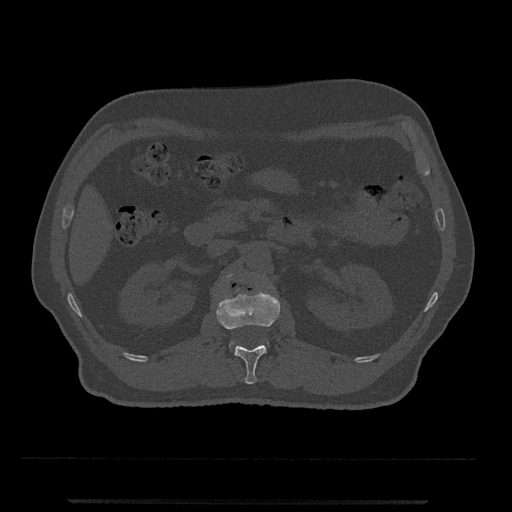
CT including the spine, one axial slice; position 314 of 797 along the scan axis; reconstruction kernel Br40s/3; 120 kVp; bone window (W 1800 / L 400 HU); 0.5 mm slice thickness; 512 × 512 image matrix. Male patient, age 63 years. Case-level facts recorded for this patient, not image findings: primary cancer: prostate.
Outlined on this slice (semi-automatically segmented with operator editing):
- L1 vertebra: box from (x=216, y=288) to (x=280, y=384) px
- L2 vertebra: (x=227, y=274)–(x=268, y=347)